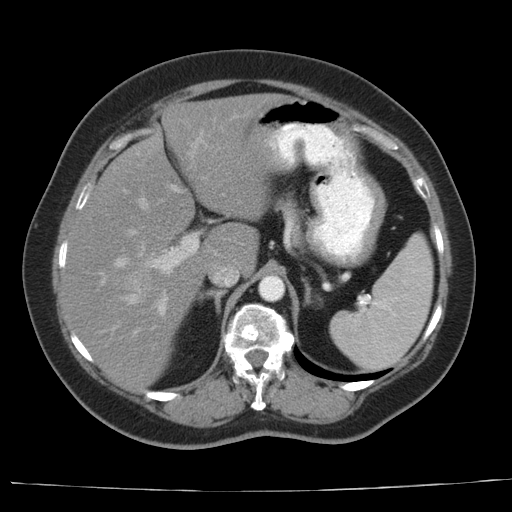
Contrast-enhanced abdominal CT, one axial slice. Reconstruction kernel AA-1. 140 kVp. Intravenous contrast given. Soft-tissue window (W 400 / L 40 HU). 5 mm slice thickness. 512 × 512 image matrix. Female patient. Case-level facts recorded for this patient, not image findings: diagnosis: colorectal cancer liver metastases, imaged before liver resection; multiple liver metastases: yes; largest metastasis: 1.8 cm; chemotherapy before resection: yes.
Outlined on this slice (manually delineated by an expert):
- hepatic veins: box from (x=127, y=199) to (x=146, y=304) px
- liver: (x=61, y=93)–(x=287, y=390)
- planned liver remnant (the part of the liver to remain after resection): (x=104, y=93)–(x=287, y=274)
- portal vein (with intrahepatic branches): (x=99, y=113)–(x=246, y=330)